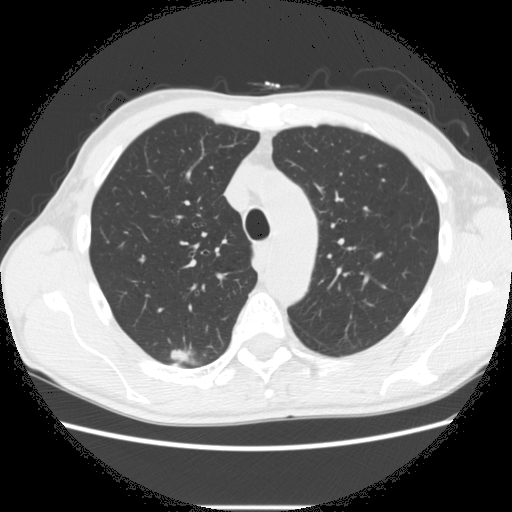
Low-dose screening chest CT, one axial slice. Slice 209 of 282 in the series (ordered by position). Reconstruction kernel STANDARD. 120 kVp. Lung window (W 1500 / L -600 HU). 512 × 512 image matrix.
Annotated regions visible in this slice (manually delineated by an expert):
- lesion 1 (tumor, upper lobe of right lung): bounding box [x1, y1, x2, y2] px = [170, 348, 189, 363]